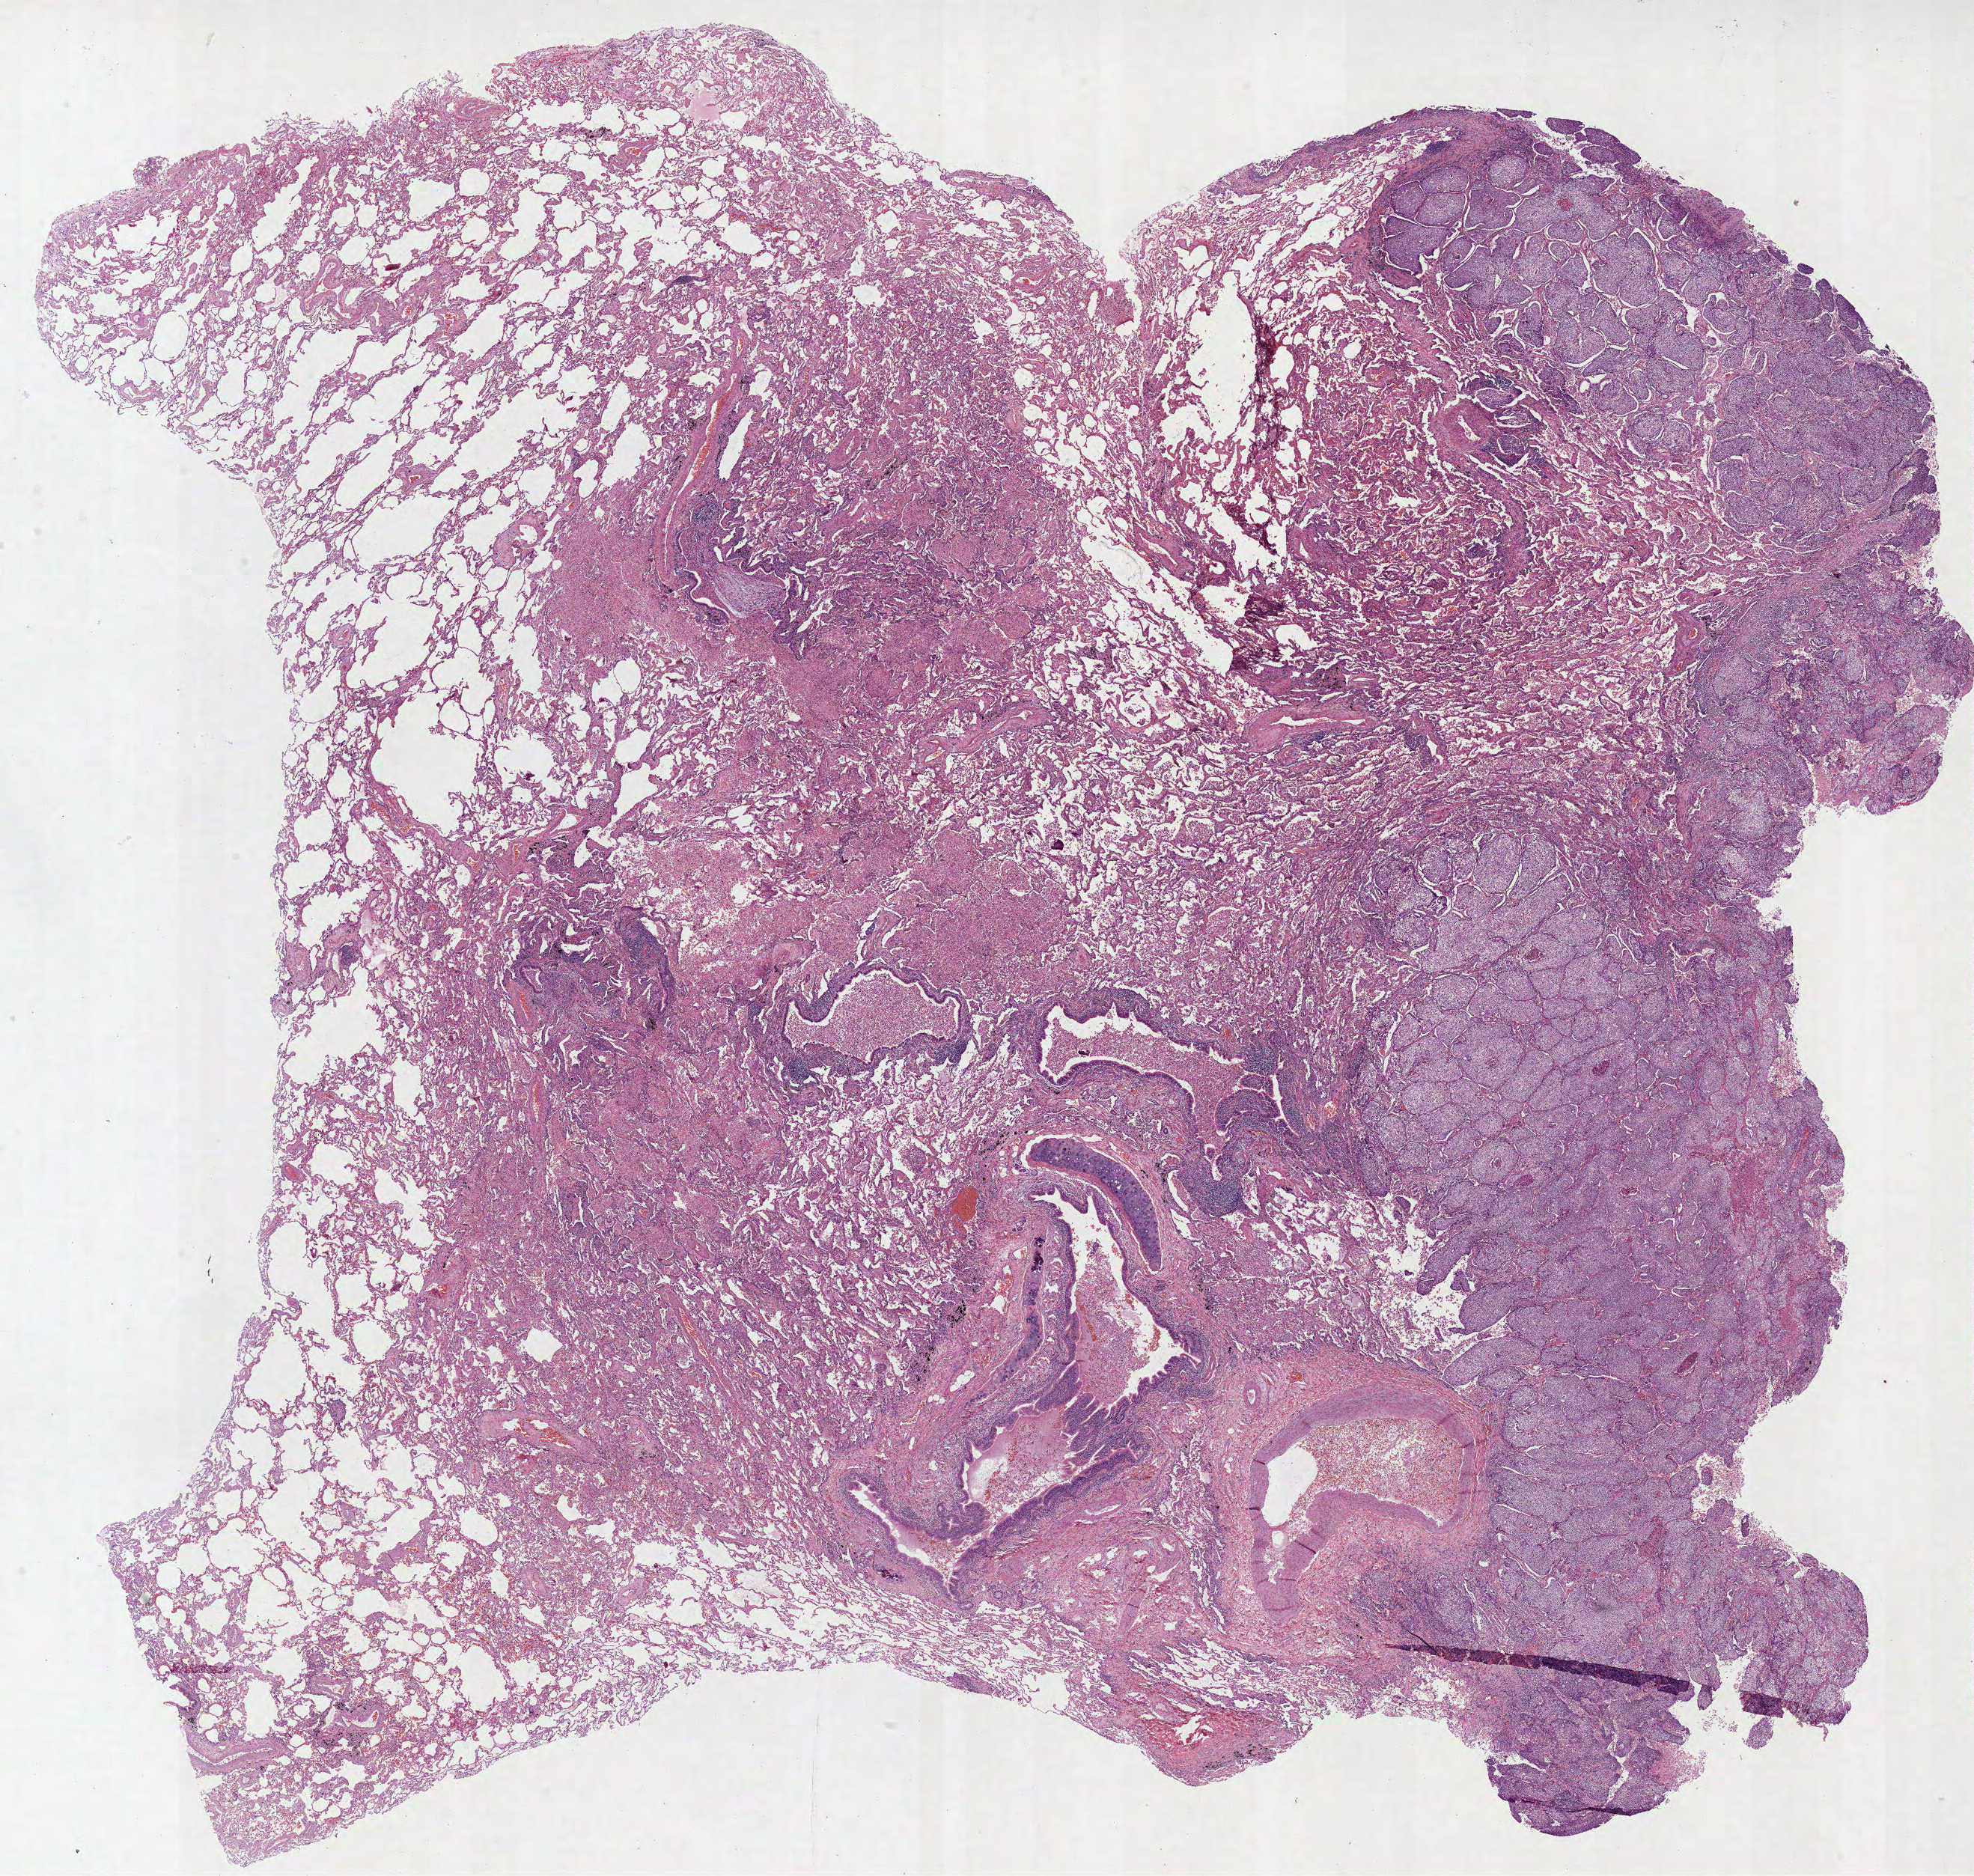
H&E-stained whole-slide image, a low-resolution overview of the entire scanned area, about 21.3 x 20.2 mm (slide scanned at 40x). Formalin-fixed paraffin-embedded (FFPE) diagnostic section. Lung, primary tumour sample. Male, age 67 years at initial diagnosis.
* AJCC pathologic stage: IIIA (7th edition)
* histologic diagnosis: Squamous cell carcinoma, NOS (upper lobe, lung)